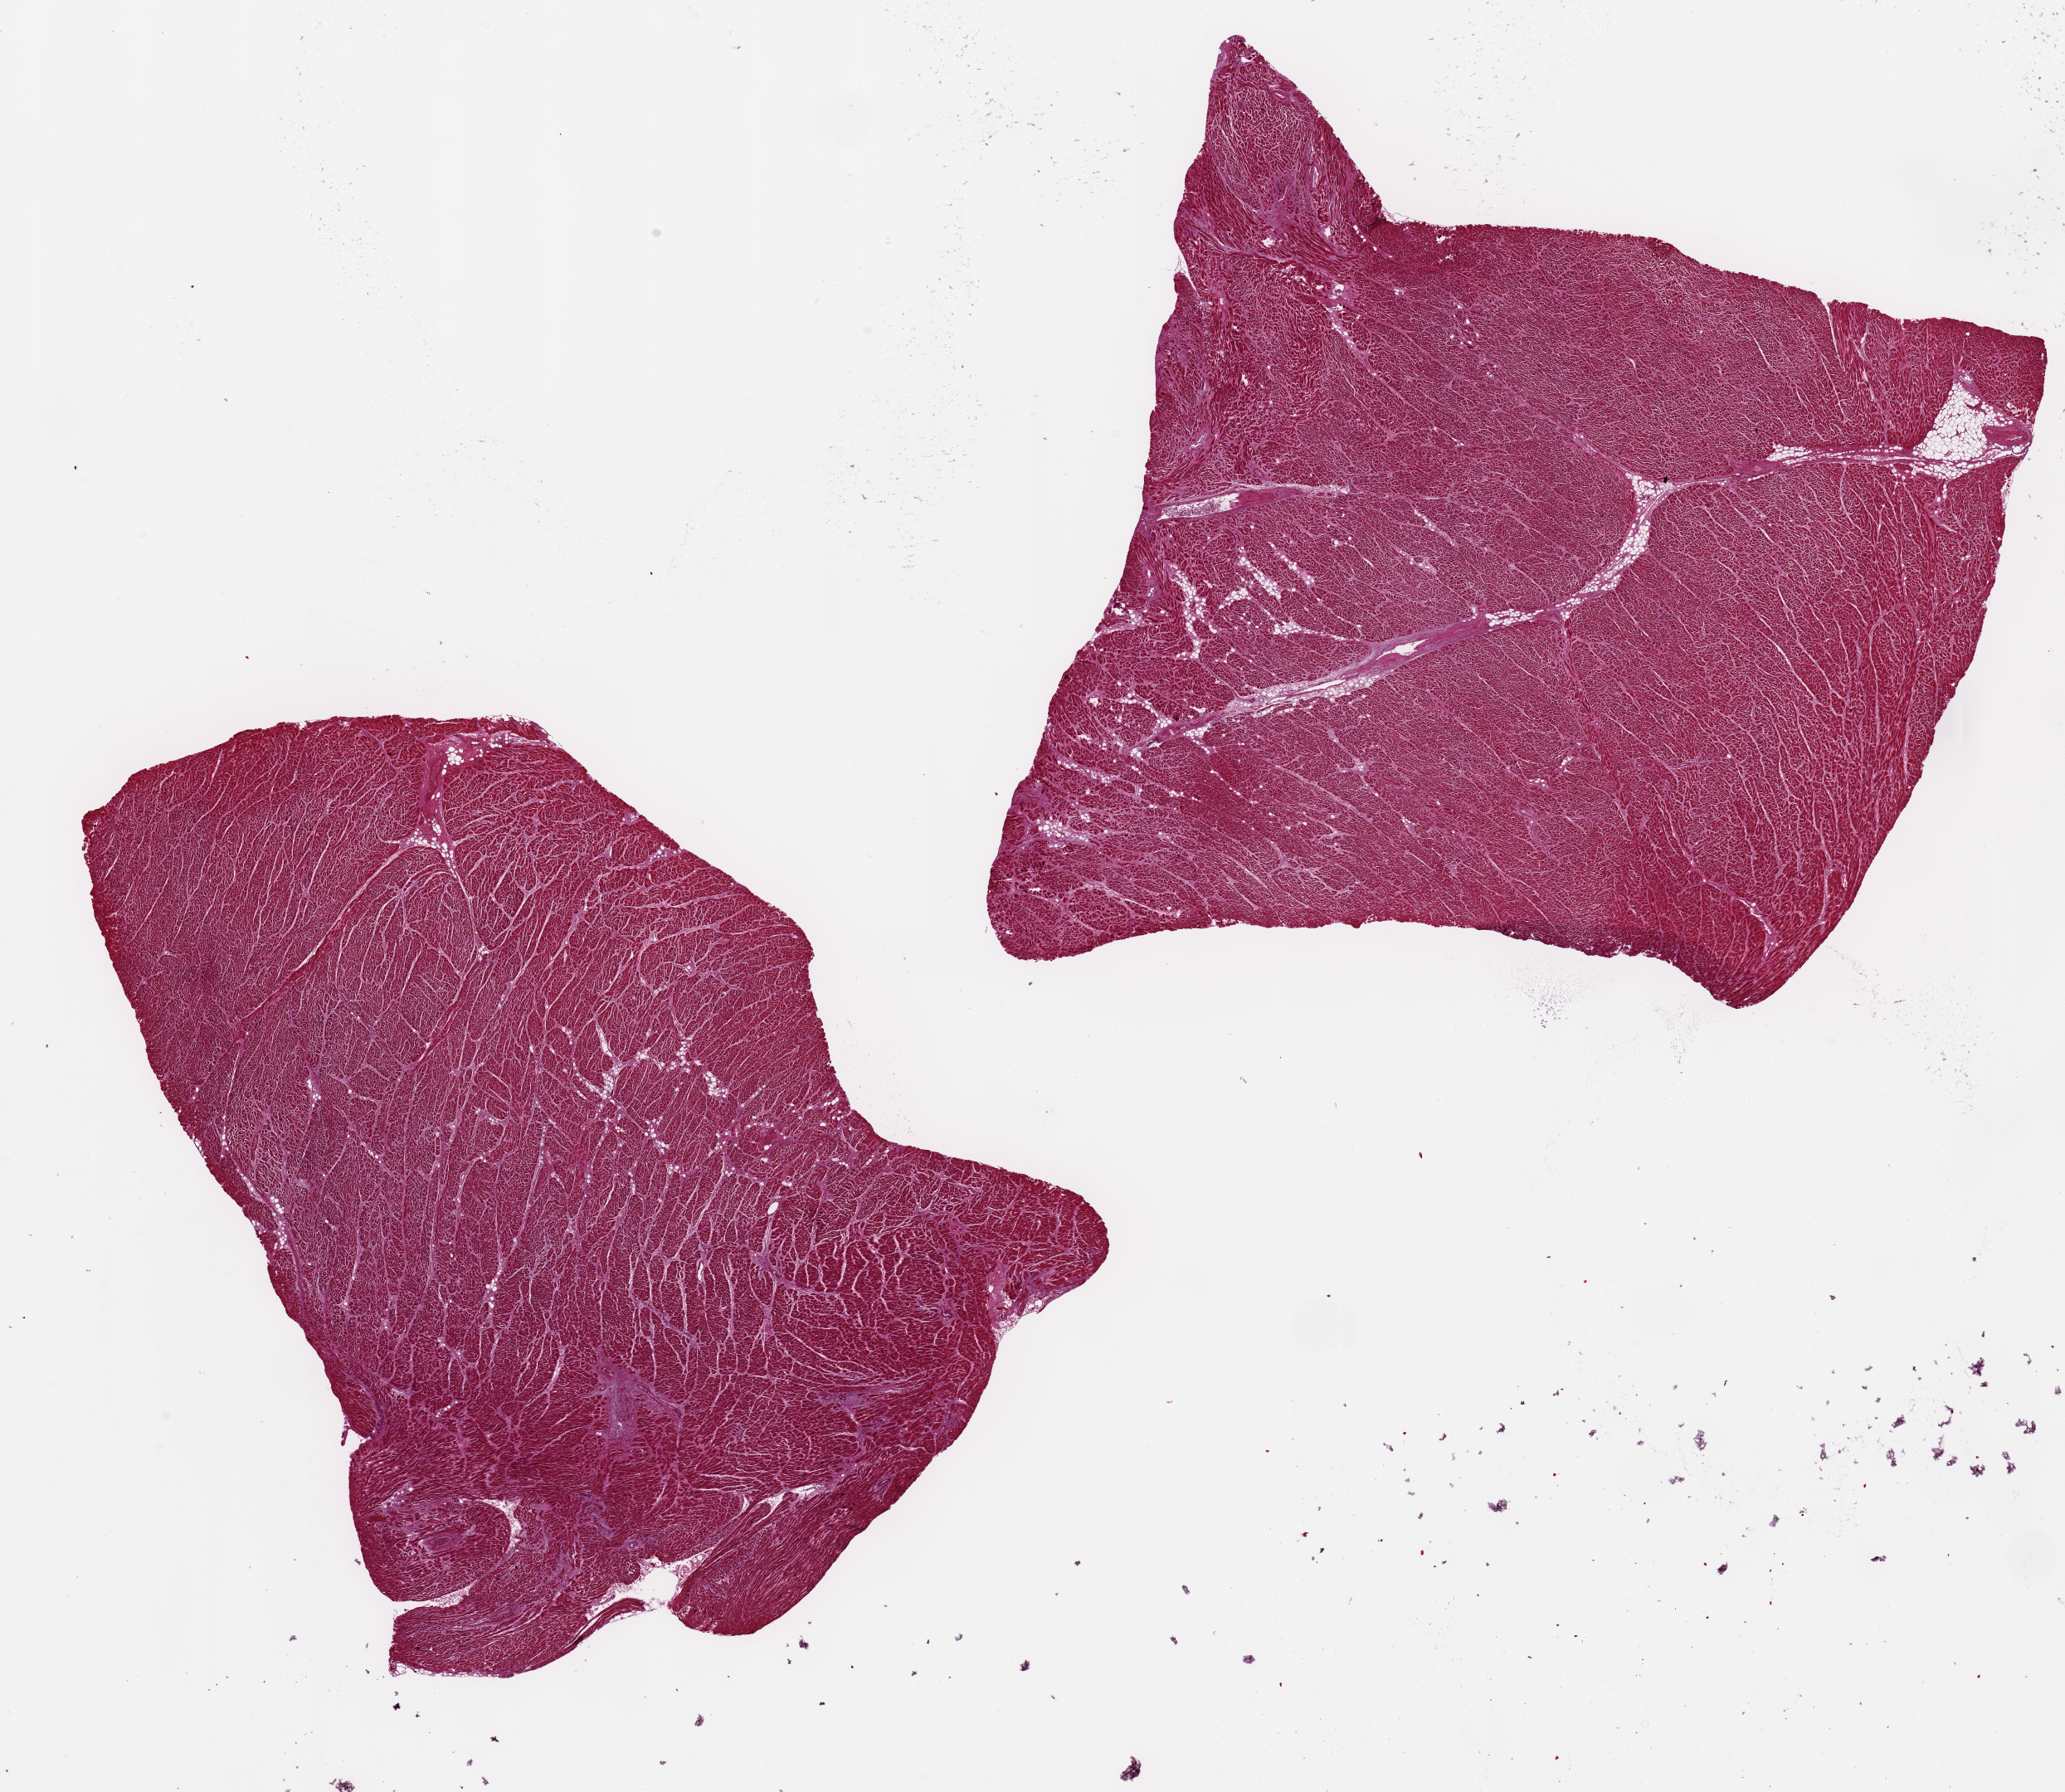
Digitized hematoxylin and eosin (H&E)-stained section, low-resolution overview of the scanned area, about 19.7 x 17.1 mm (acquisition: 20x scan); PAXgene-fixed, paraffin-embedded tissue; section of heart (target tissue); tissue donor sample.
- review note (as recorded): 2 pieces 9x8 & 8x8 mm; moderate interstitial fibrosis